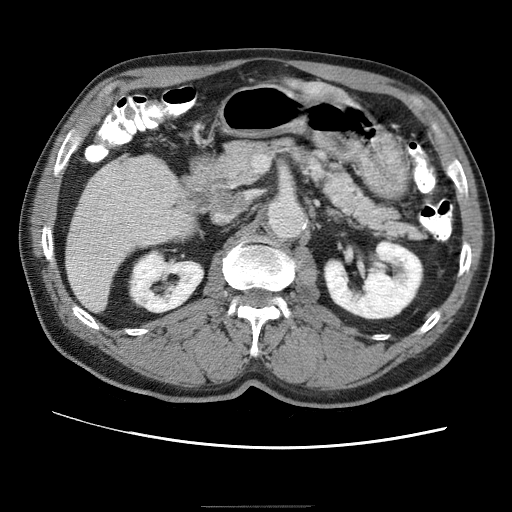
Contrast-enhanced abdominal CT (liver protocol), one axial slice. Position 16 of 75 along the scan axis. 120 kVp. One of 2 acquisitions stored at this slice position. Soft-tissue window (W 400 / L 40 HU). 512 × 512 image matrix. From the clinical record (not read from this slice): diagnosis: hepatocellular carcinoma (patient treated with transarterial chemoembolisation; whether this scan precedes or follows treatment is not stated here); TNM stage (as recorded): Stage-II; Child-Pugh class: A; tumour nodularity: multinodular; tumour size: 2 cm.
Structures marked on this image (semi-automatic segmentation, software-assisted and operator-edited):
- liver parenchyma outside the tumour (the mass and vessels are separate outlines, so this box may not span the whole liver): bounding box [x1, y1, x2, y2] px = [66, 158, 170, 308]
- liver vessels: [79, 162, 114, 277]